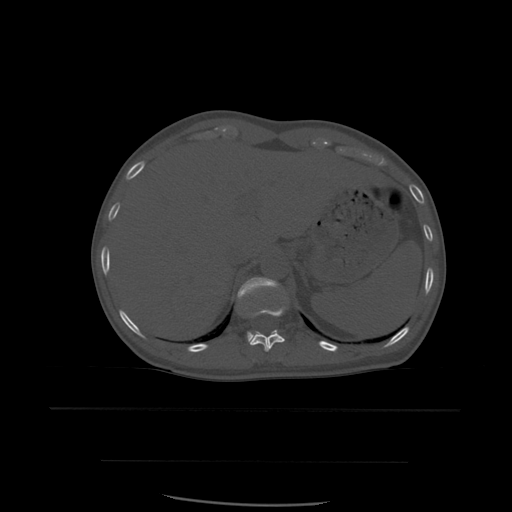
CT including the spine, one axial slice; position 289 of 574 along the scan axis; bone window (W 1800 / L 400 HU); 1.25 mm slice thickness; 512 × 512 image matrix. Patient age 48 years. Case-level facts recorded for this patient, not image findings: primary cancer: lung.
Outlined on this slice (semi-automatically segmented with operator editing):
- T11 vertebra: box from (x=247, y=305) to (x=287, y=352) px
- T12 vertebra: (x=238, y=277)–(x=281, y=341)